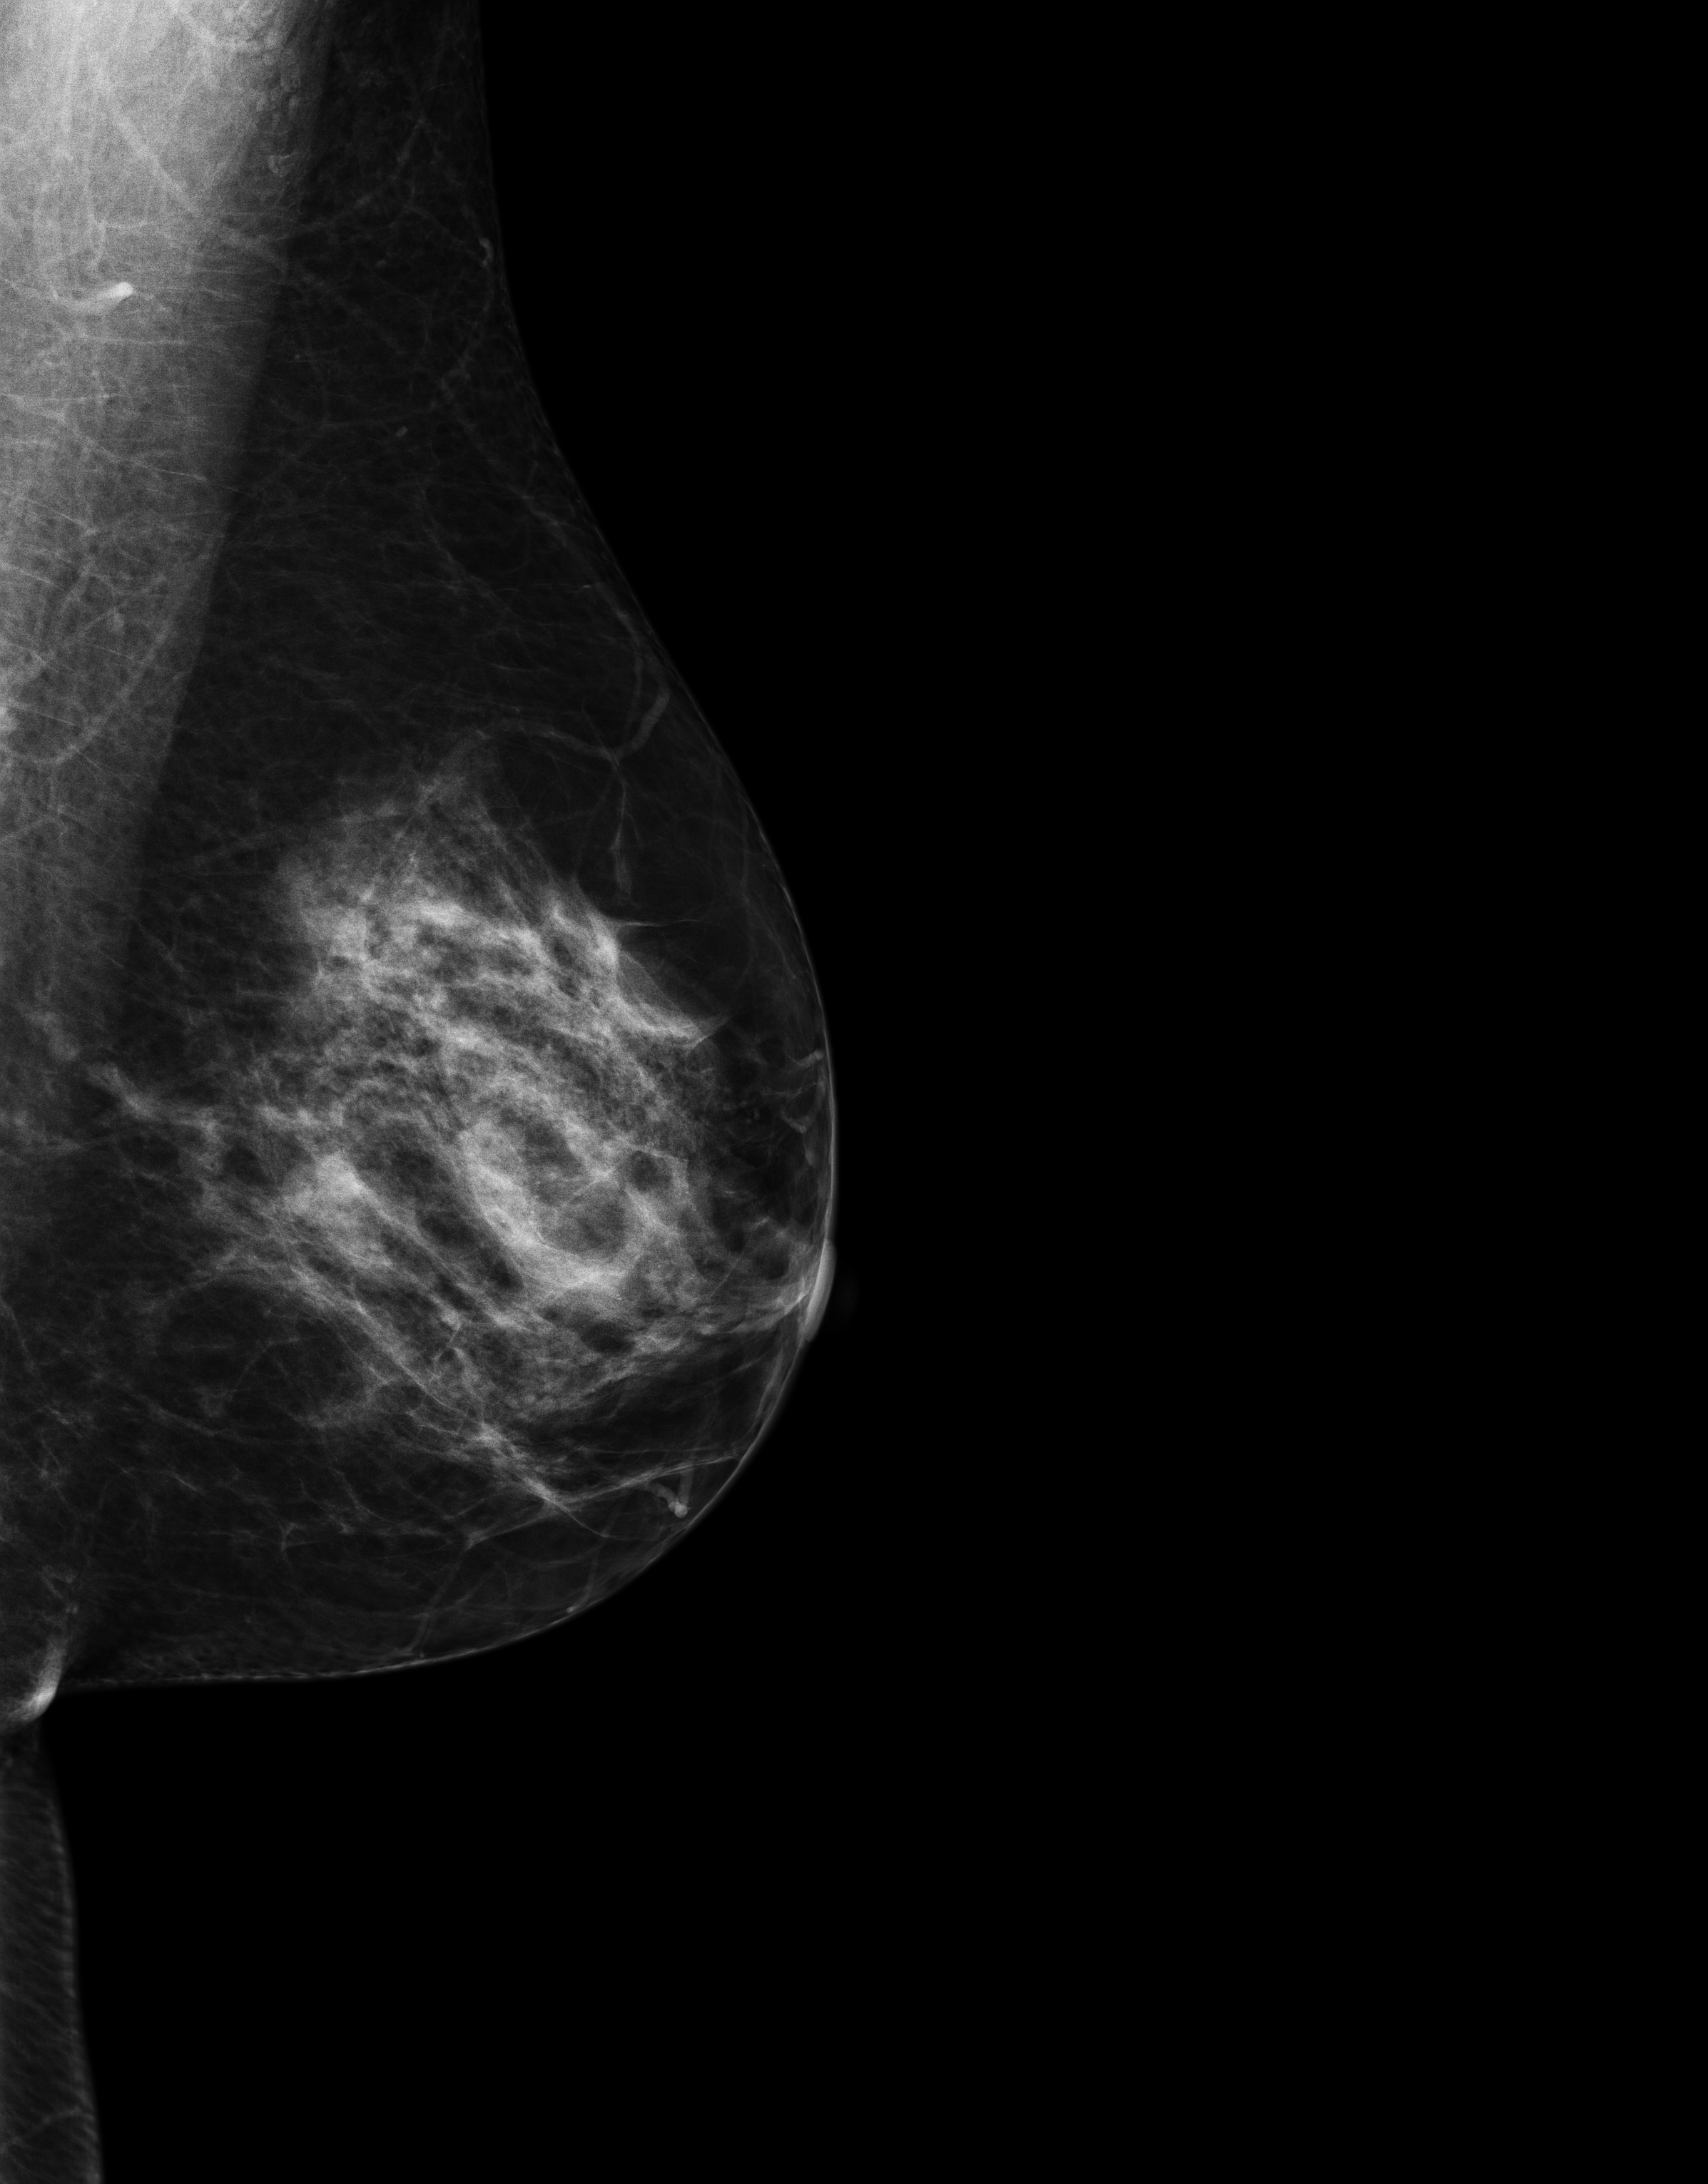
Screening examination. Patient: female, 46 years.
Image type: full-field digital mammogram. Breast: left. Projection: medio-lateral oblique projection.